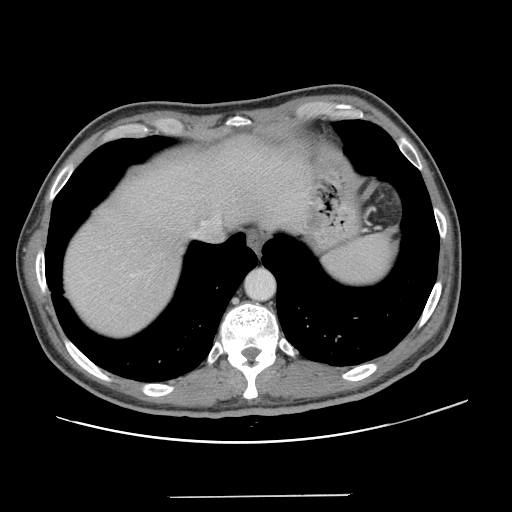
Contrast-enhanced abdominal CT, one axial slice; position 114 of 131 along the scan axis; intravenous contrast given; soft-tissue window (W 400 / L 40 HU); 512 × 512 image matrix, field of view 403 × 403 mm. Male patient, age 60 years. Case-level facts recorded for this patient, not image findings: diagnosis: colorectal cancer liver metastases, imaged before liver resection; multiple liver metastases: no; largest metastasis: 2.5 cm; chemotherapy before resection: no.
Structures marked on this image (manually delineated by an expert):
- hepatic veins: bounding box (x1, y1, x2, y2) in pixels: (155, 204, 216, 237)
- liver: (63, 137, 304, 338)
- planned liver remnant (the part of the liver to remain after resection): (63, 137, 305, 335)